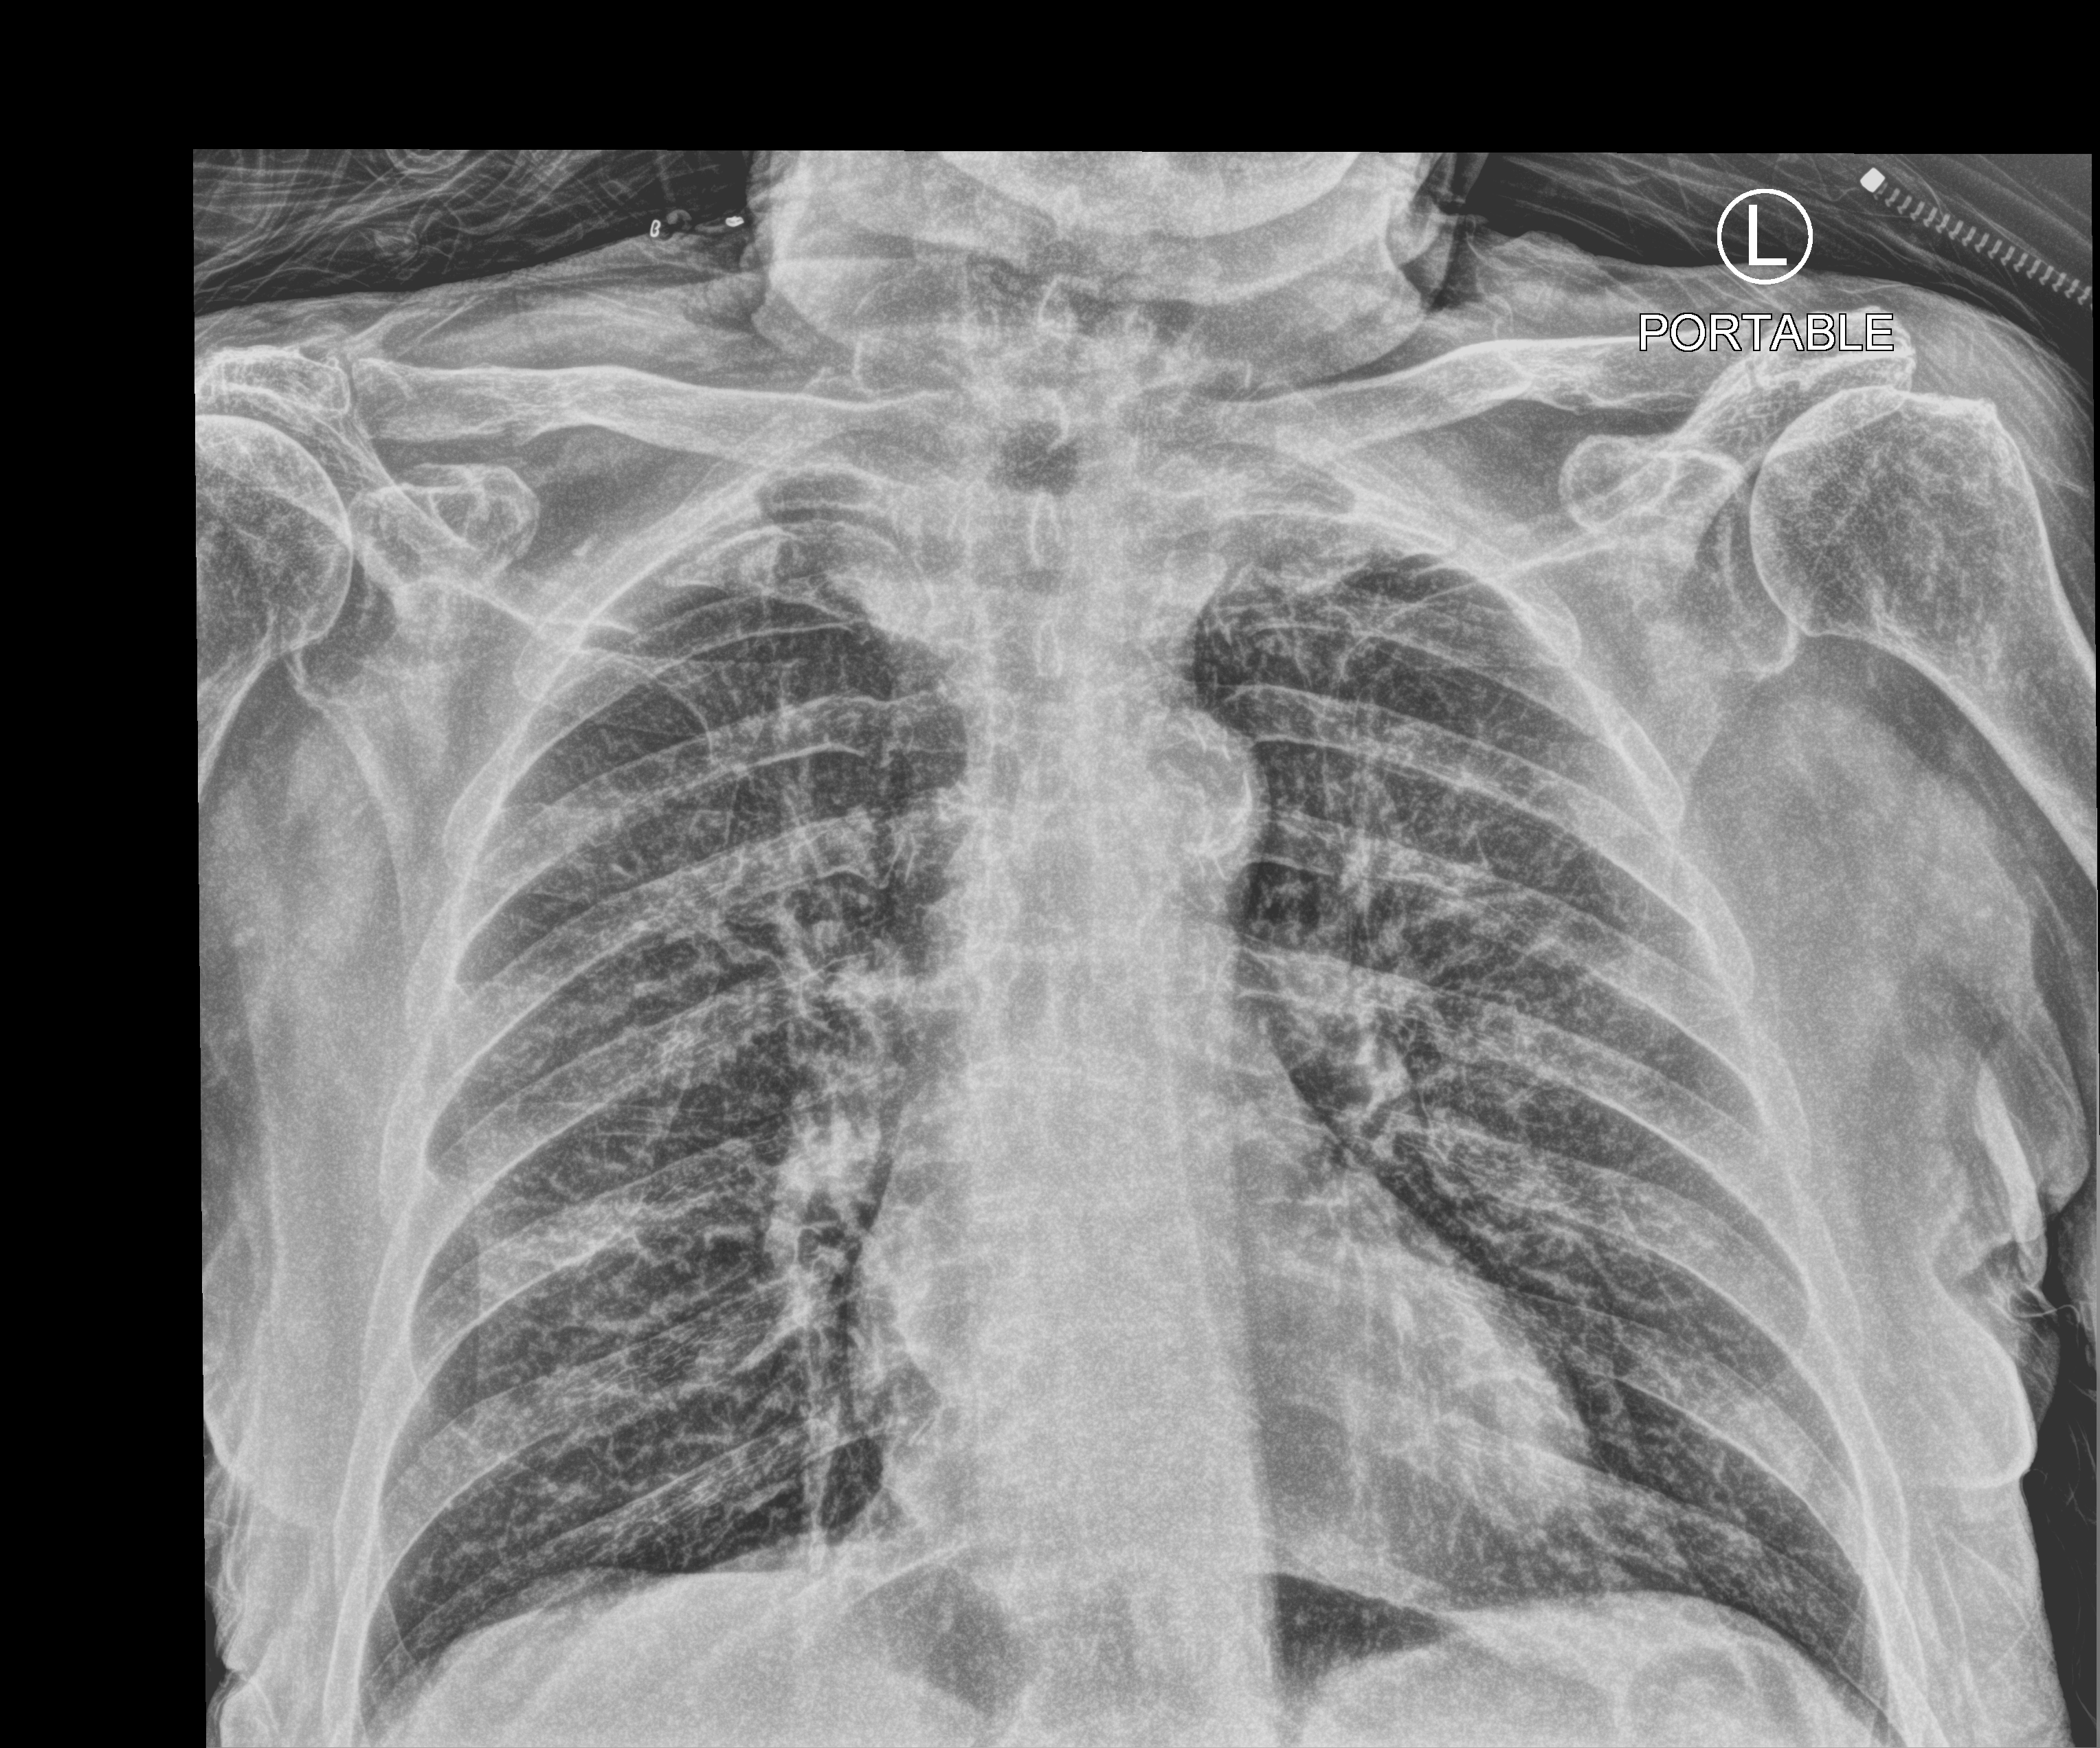
Portable chest radiograph, anteroposterior (AP) projection. Patient hospitalised with COVID-19; male, aged 75–90 years.
Admission-level facts for this patient (not findings on this image; timing relative to this image not recorded): hypertension (admission record): yes.